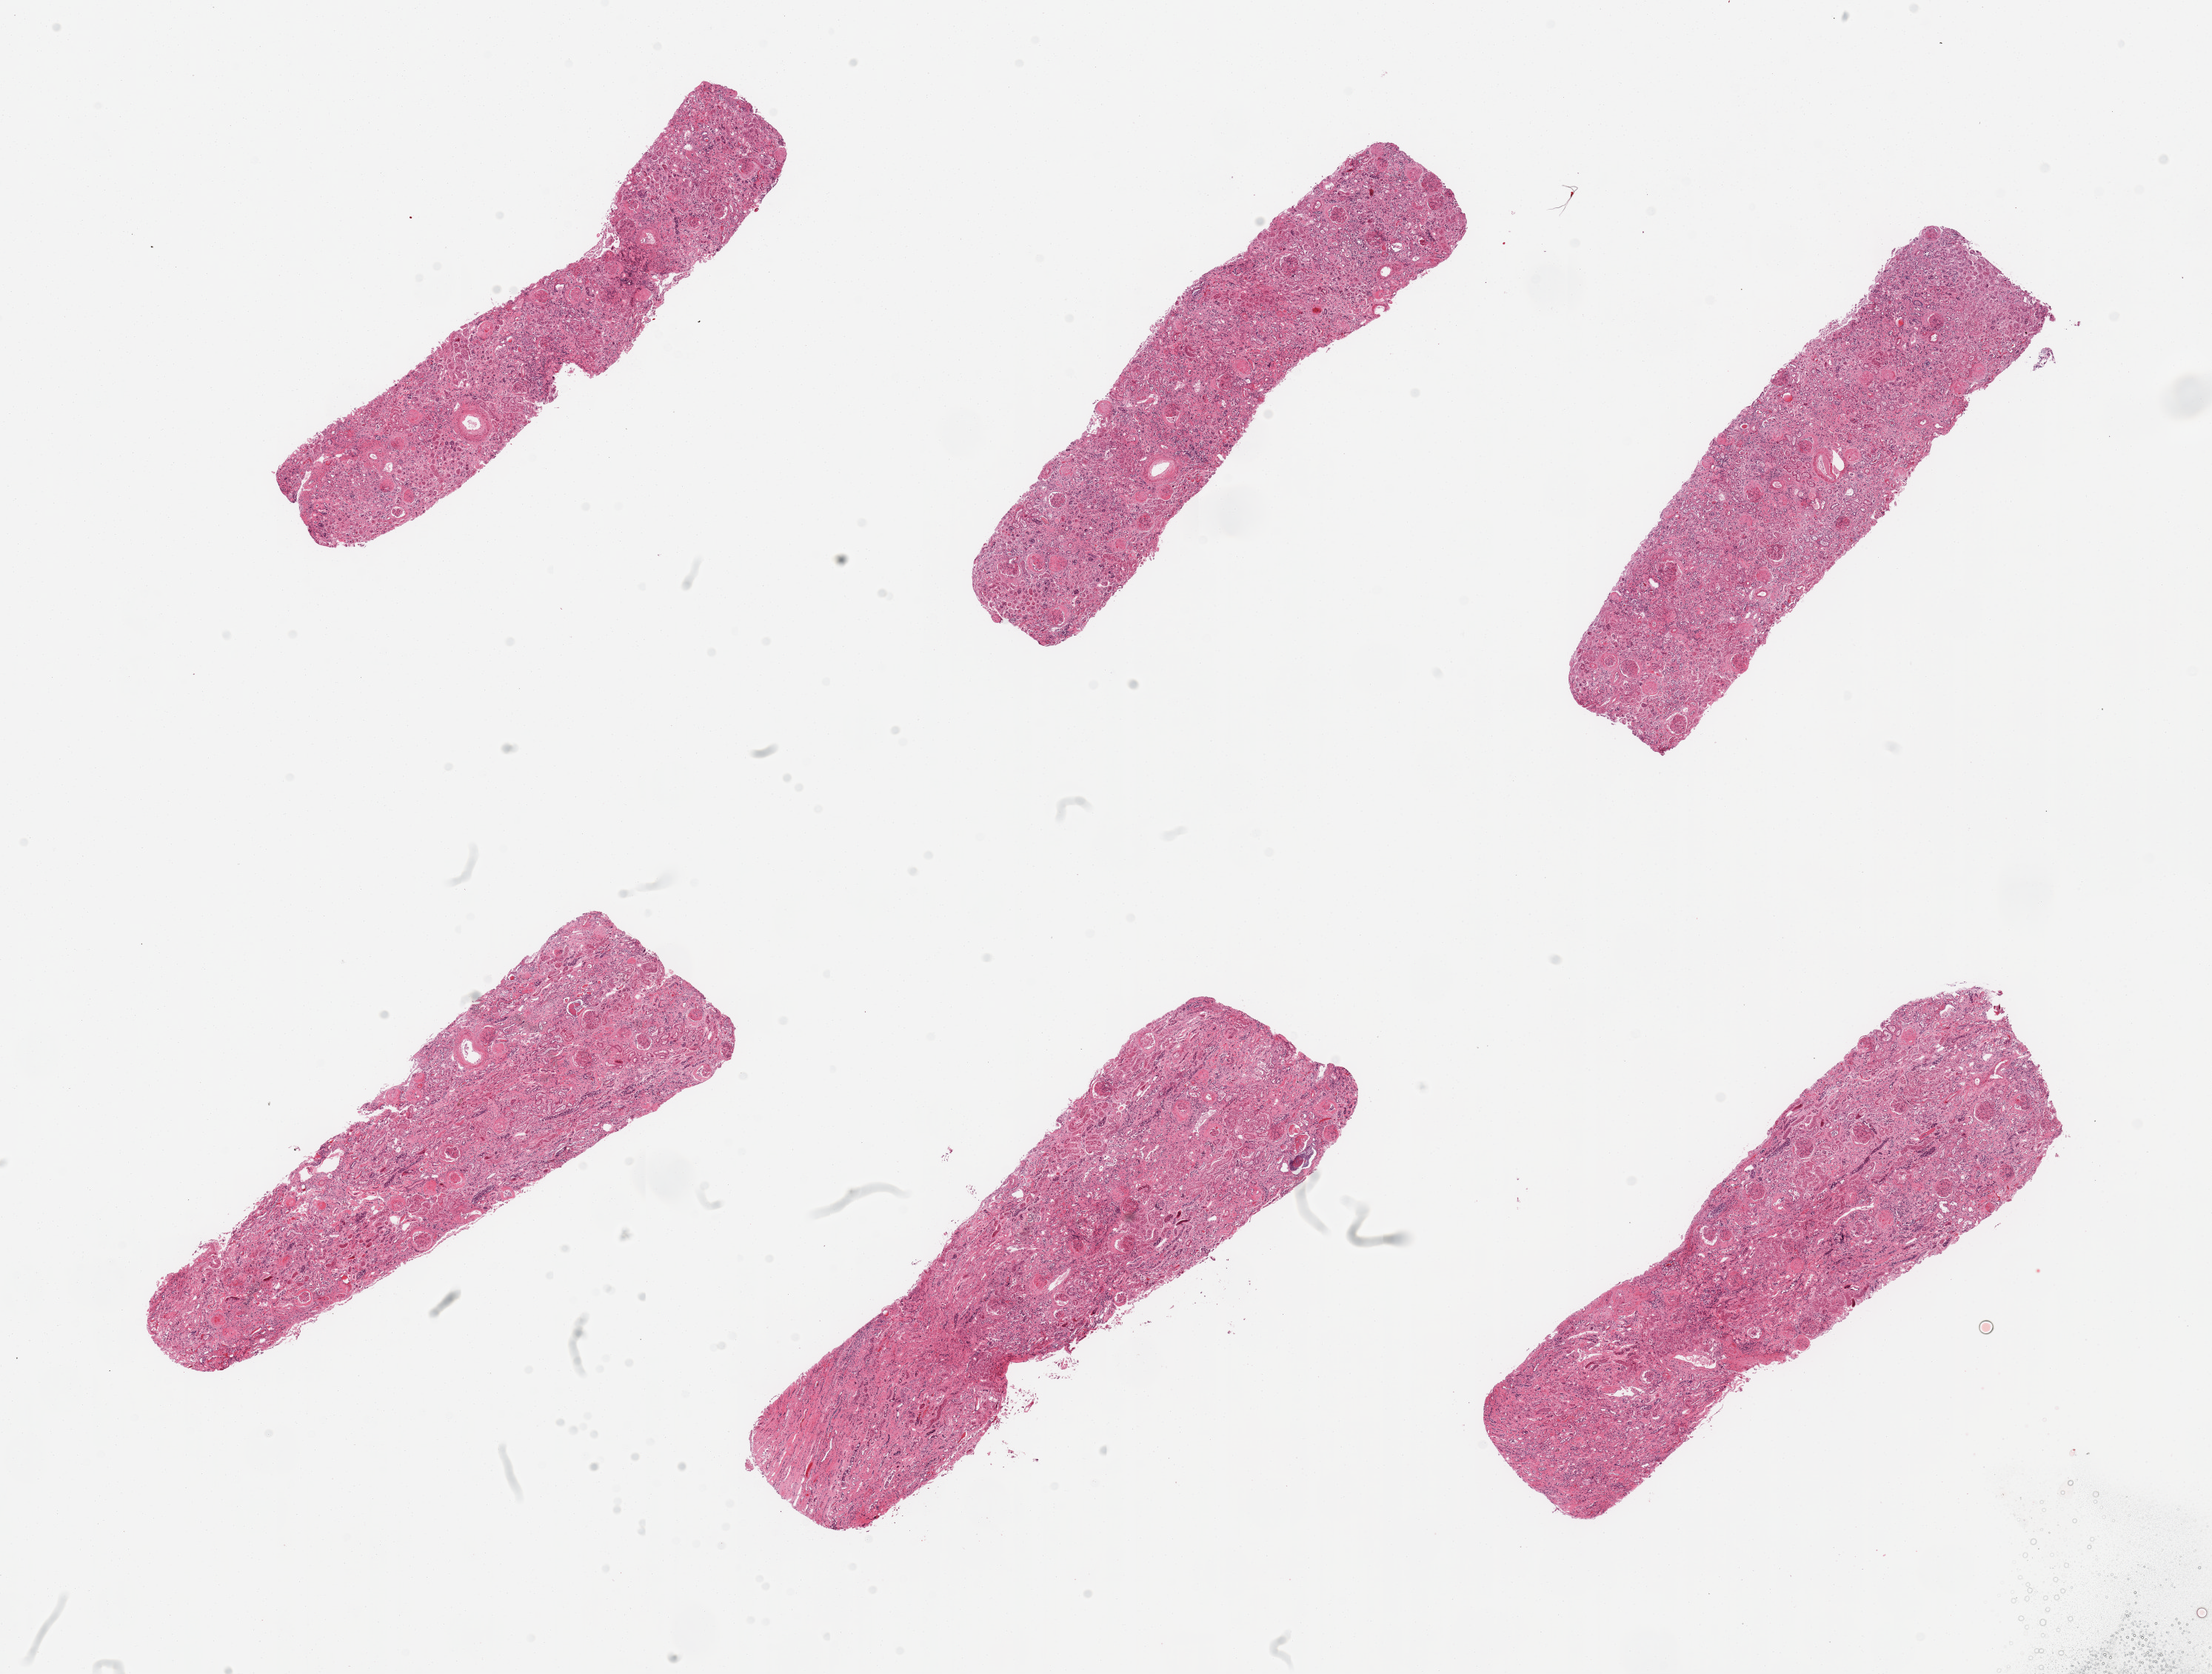
H&E whole-slide image, low-resolution overview of the scanned area, about 23.6 x 17.9 mm (acquisition: 20x scan); PAXgene-fixed paraffin-embedded (PFPE) section; section of renal cortex (target tissue); donor tissue sample. Donor: male.
Reviewer comment on this tissue sample: 6 pieces, markedd glomerulosclerosis; tubules badly autolyzed.